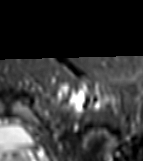
MRI of an extremity soft-tissue mass, one axial slice. Slice 60 of 81 in the series (ordered by position). STIR. MR volume resampled by the dataset authors to the PET/CT grid (not the native acquisition matrix). 143 × 161 image matrix. Female patient. From the clinical record (not read from this slice): histological type: myxofibrosarcoma; grade: intermediate; site of the primary tumour: left thigh.
Annotated regions visible in this slice (expert contour drawn on MRI and transferred to this co-registered scan by the dataset authors):
- gross tumour volume including surrounding oedema: box from (x=60, y=85) to (x=107, y=105) px